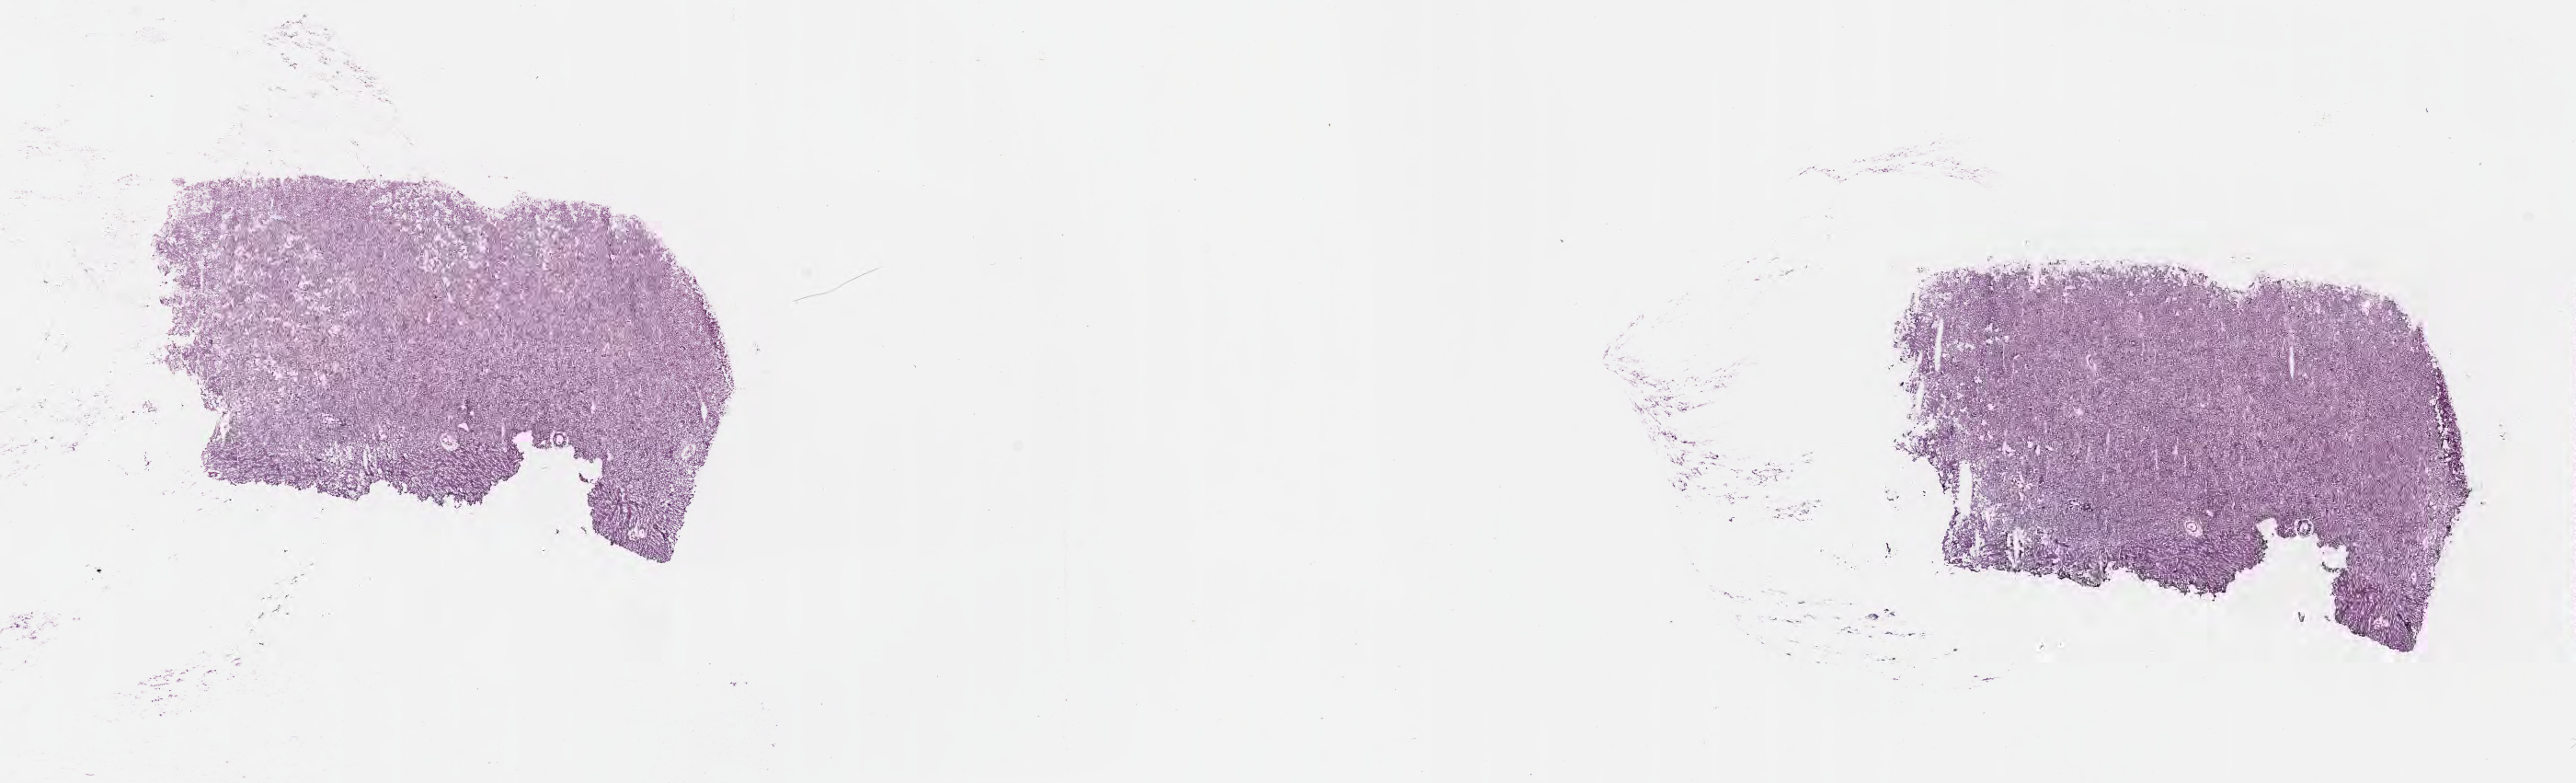
Digitized hematoxylin and eosin (H&E)-stained section, low-resolution overview of the scanned area, about 22.6 x 6.9 mm; frozen section; primary tumor; anatomic site: spleen. Patient female; 15 years old. Slide review estimates, as recorded: tumor cells 5%, tumor nuclei 10%, stromal cells 5%, necrosis 90%, normal cells 0%. Inflammatory infiltration, as recorded: lymphocyte infiltration 5%, monocyte infiltration 5%, neutrophil infiltration 0%.
Diagnosis: Burkitt lymphoma, NOS. Ann Arbor stage (patient): Stage III. Section: bottom of the tissue portion.